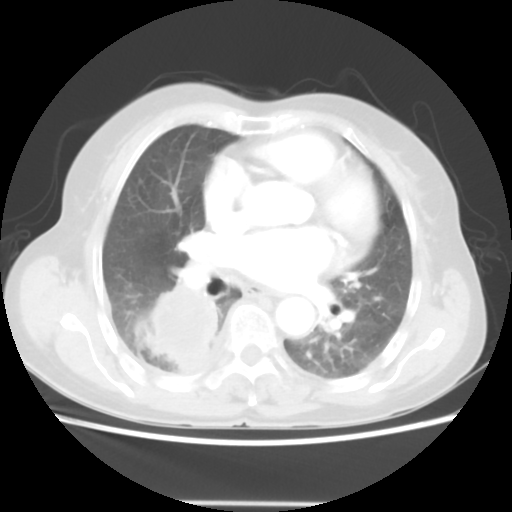
Chest CT, one axial slice; reconstruction kernel STANDARD; 140 kVp; lung window (W 1500 / L -600 HU); 5 mm slice thickness; 512 × 512 image matrix, field of view 337 × 337 mm. Patient: female, 67 years. From the clinical record (not read from this slice): clinical TNM (as recorded): T3 N1 M1.
Annotated regions visible in this slice (rectangle marked by the reading radiologist):
- lung tumour (recorded histology: adenocarcinoma): bounding box [x1, y1, x2, y2] px = [142, 281, 222, 383]